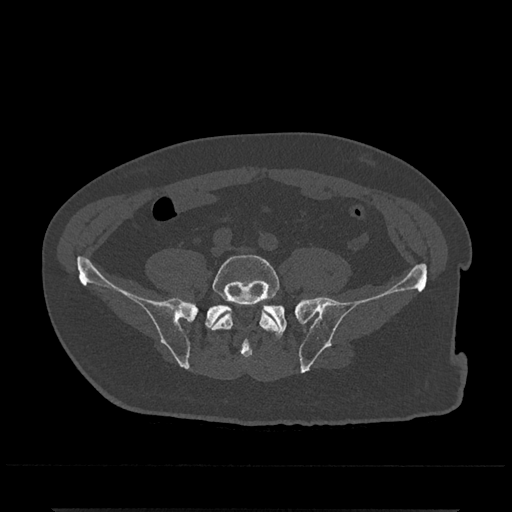
CT including the spine, one axial slice. Slice 65 of 797 in the series (ordered by position). Reconstruction kernel Br40s/3. Bone window (W 1800 / L 400 HU). 0.5 mm slice thickness. 512 × 512 image matrix, field of view 393 × 393 mm. Male patient, age 67 years. Case-level facts recorded for this patient, not image findings: primary cancer: prostate.
Annotated regions visible in this slice (semi-automatically segmented with operator editing):
- L5 vertebra: bounding box <210,254,280,355> (left, top, right, bottom; pixels)